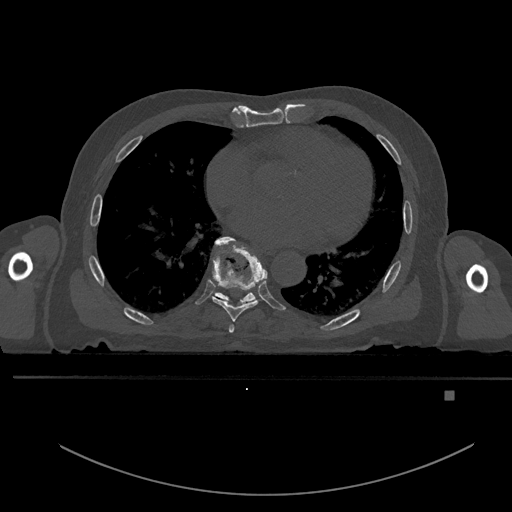
CT including the spine, one axial slice. Position 237 of 969 along the scan axis. Bone window (W 1800 / L 400 HU). 0.5 mm slice thickness. 512 × 512 image matrix, field of view 456 × 456 mm. Male patient, age 82 years. From the clinical record (not read from this slice): primary cancer: prostate.
Structures marked on this image (semi-automatic segmentation, software-assisted and operator-edited):
- T6 vertebra: box from (x=228, y=324) to (x=235, y=333) px
- T7 vertebra: (x=211, y=236)–(x=267, y=321)
- T8 vertebra: (x=211, y=240)–(x=256, y=305)